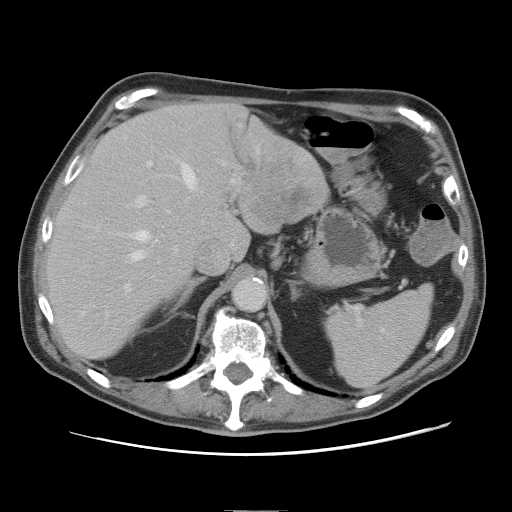
Contrast-enhanced abdominal CT, one axial slice; slice 54 of 89 in the series (ordered by position); 120 kVp; intravenous contrast given; soft-tissue window (W 400 / L 40 HU); 5 mm slice thickness; 512 × 512 image matrix, field of view 375 × 375 mm. Male patient, age 69 years. Case-level facts recorded for this patient, not image findings: diagnosis: colorectal cancer liver metastases, imaged before liver resection; multiple liver metastases: no; largest metastasis: 8.5 cm; disease in both lobes: no.
Annotated regions visible in this slice (outlined manually by an expert reader):
- hepatic veins: bounding box <127,163,198,263> (left, top, right, bottom; pixels)
- liver: <49,104,328,359>
- planned liver remnant (the part of the liver to remain after resection): <49,104,247,359>
- portal vein (with intrahepatic branches): <126,146,259,290>
- liver metastasis: <248,186,312,227>